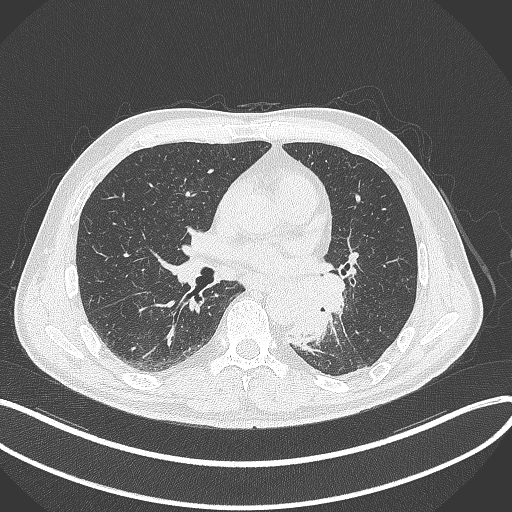
Chest CT, one axial slice; slice 166 of 329 in the series (ordered by position); 120 kVp; lung window (W 1500 / L -600 HU); 1 mm slice thickness; 512 × 512 image matrix. Patient: male, 59 years. From the clinical record (not read from this slice): clinical TNM (as recorded): T2a N2 M0.
Annotated regions visible in this slice (bounding box drawn by a radiologist):
- lung tumour (recorded histology: squamous cell carcinoma): bounding box <304,271,344,347> (left, top, right, bottom; pixels)